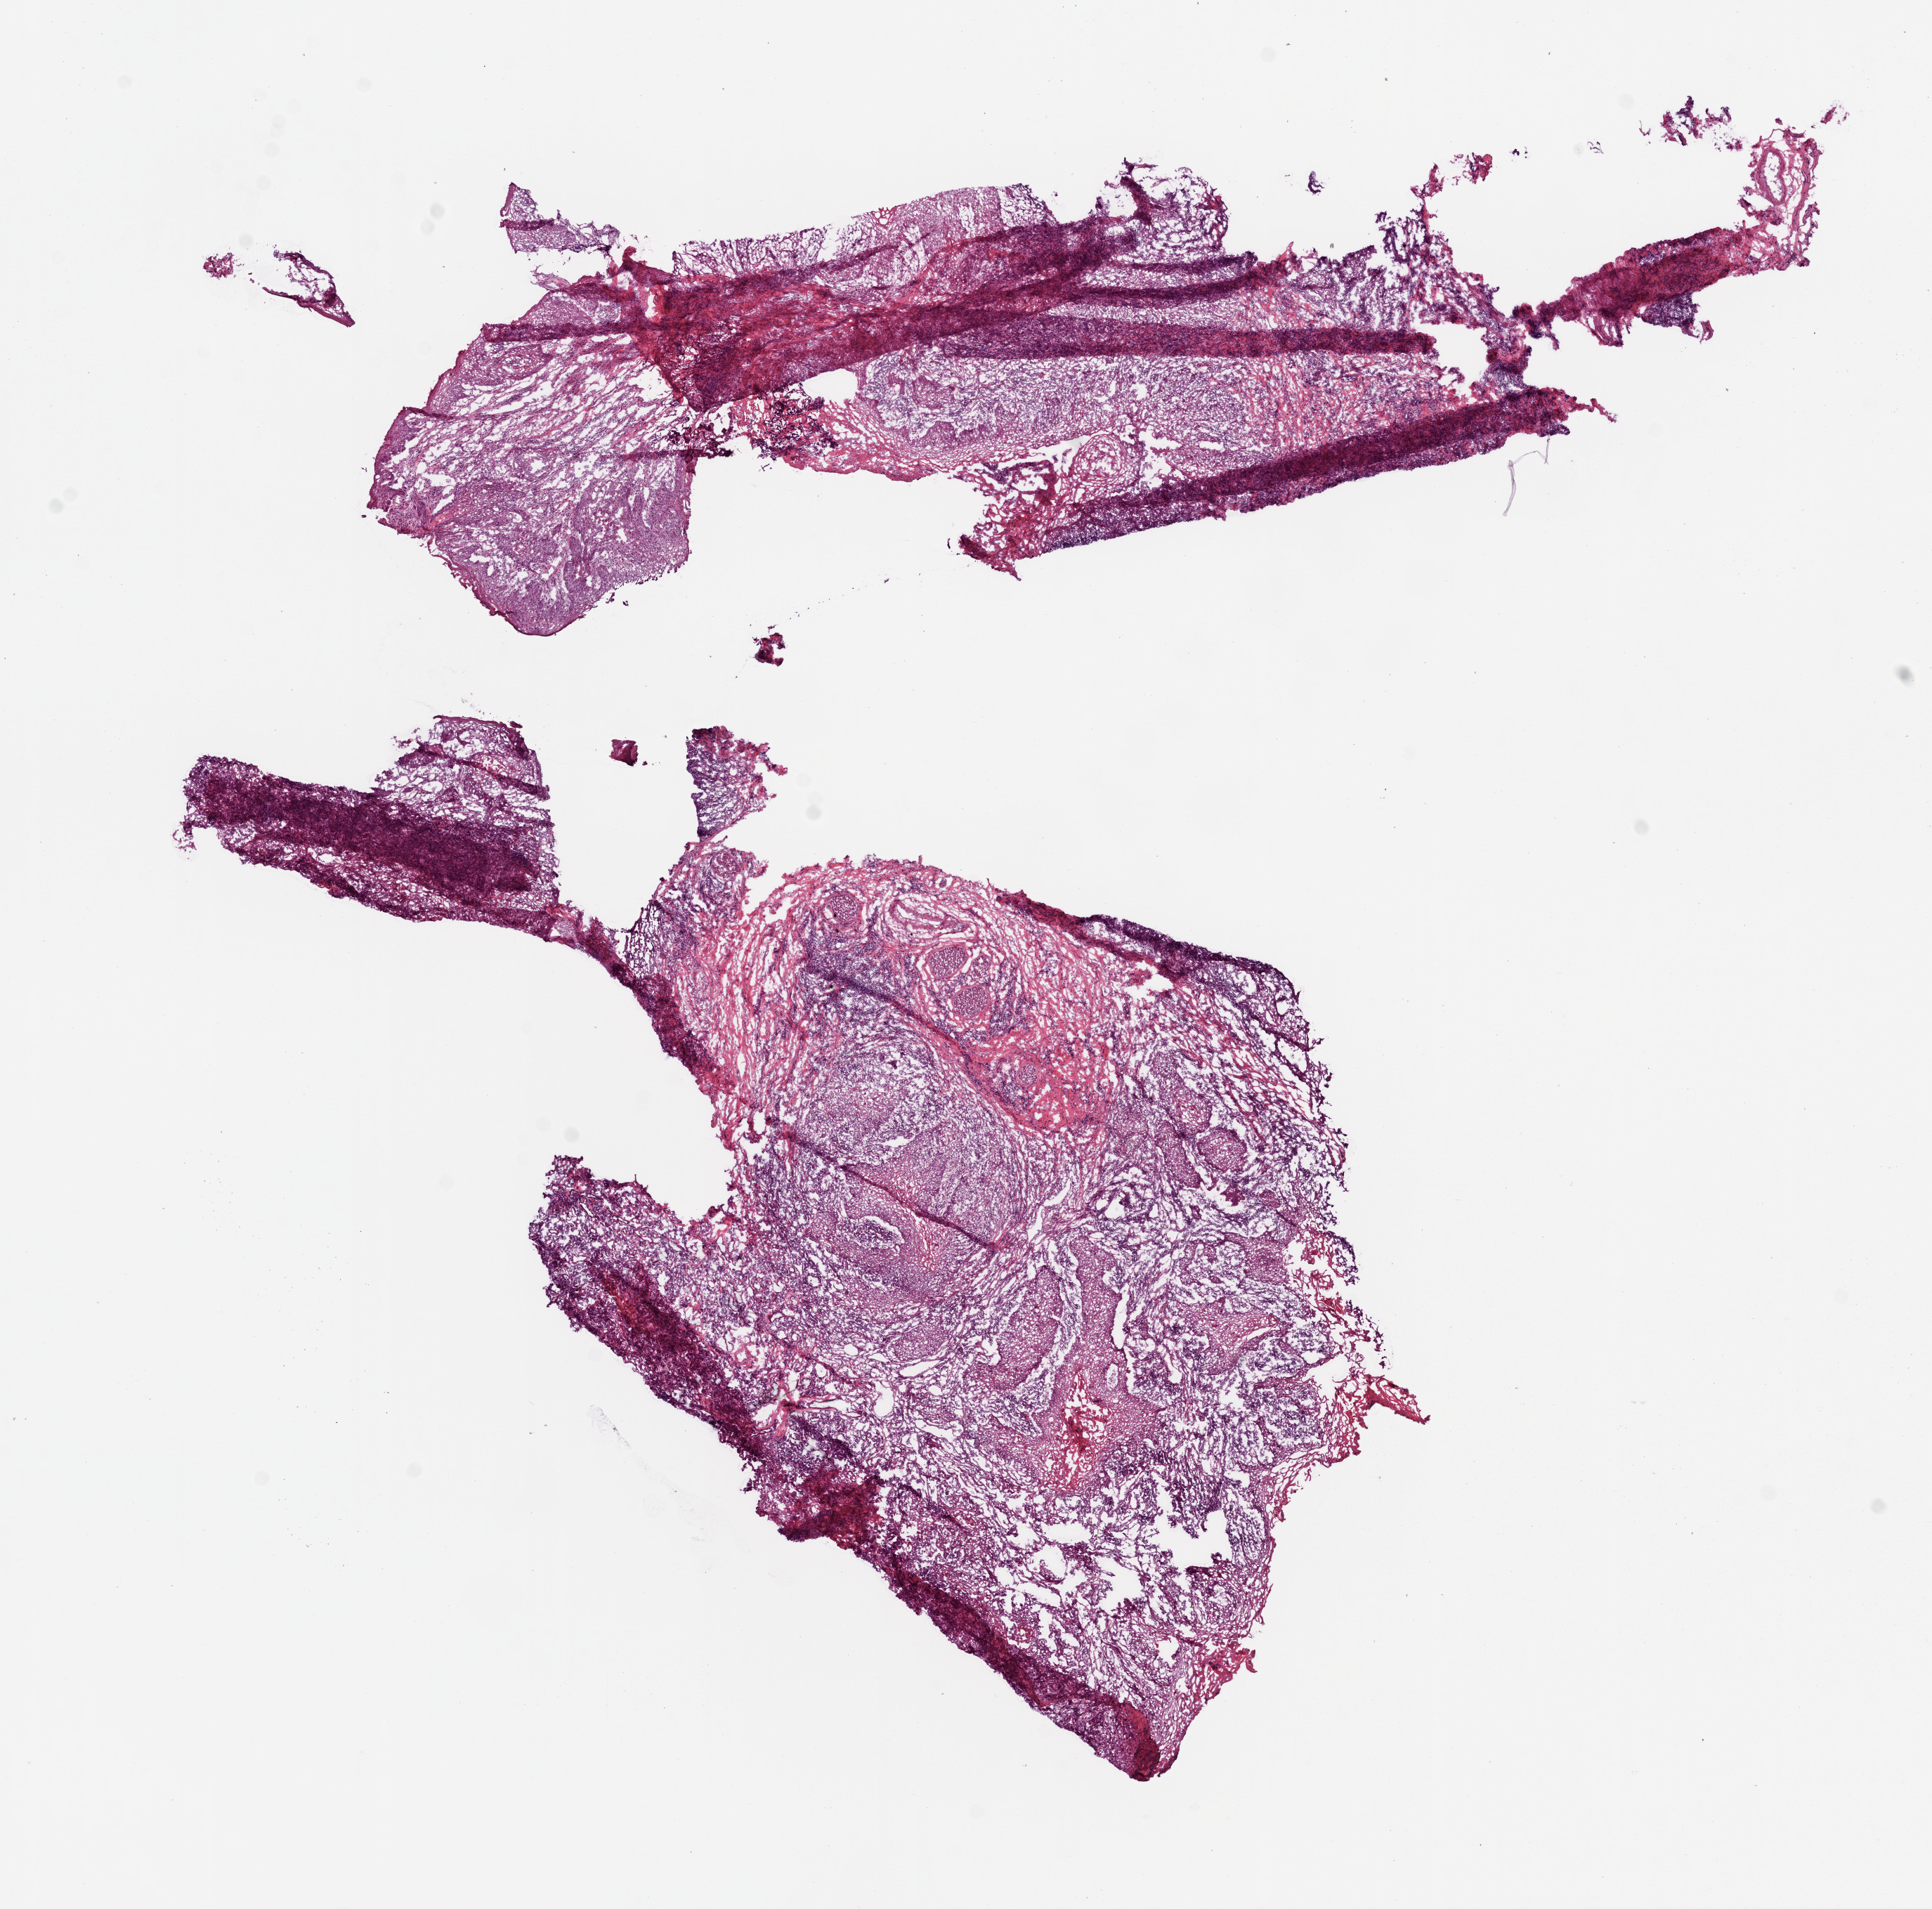
H&E-stained whole-slide image — a low-resolution overview of the entire scanned area, about 11.0 x 10.9 mm (slide scanned at 20x). Frozen section from the bottom of the tissue portion. Head and neck, primary tumour sample. Patient sex: female. Histologic grade: G3 (poorly differentiated). Composition of this section per pathologist review: tumour cells 90%, tumour nuclei 80%, normal cells 0%, stromal cells 10%, necrosis 0%.
* AJCC pathologic stage: IVA (6th edition)
* histologic diagnosis: Squamous cell carcinoma, NOS (hard palate)